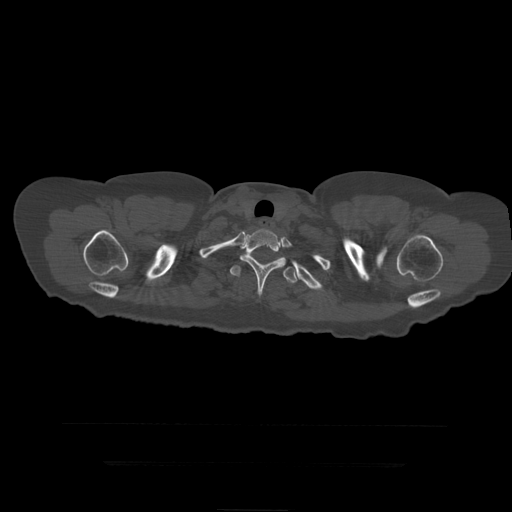
CT including the spine, one axial slice. Slice 373 of 399 in the series (ordered by position). Reconstruction kernel STANDARD. Bone window (W 1800 / L 400 HU). 512 × 512 image matrix, field of view 450 × 450 mm. Patient age 41 years. From the clinical record (not read from this slice): primary cancer: breast.
Outlined on this slice (semi-automatic segmentation, software-assisted and operator-edited):
- T2 vertebra: box from (x=240, y=229) to (x=286, y=297) px
- T3 vertebra: (x=230, y=254)–(x=298, y=284)